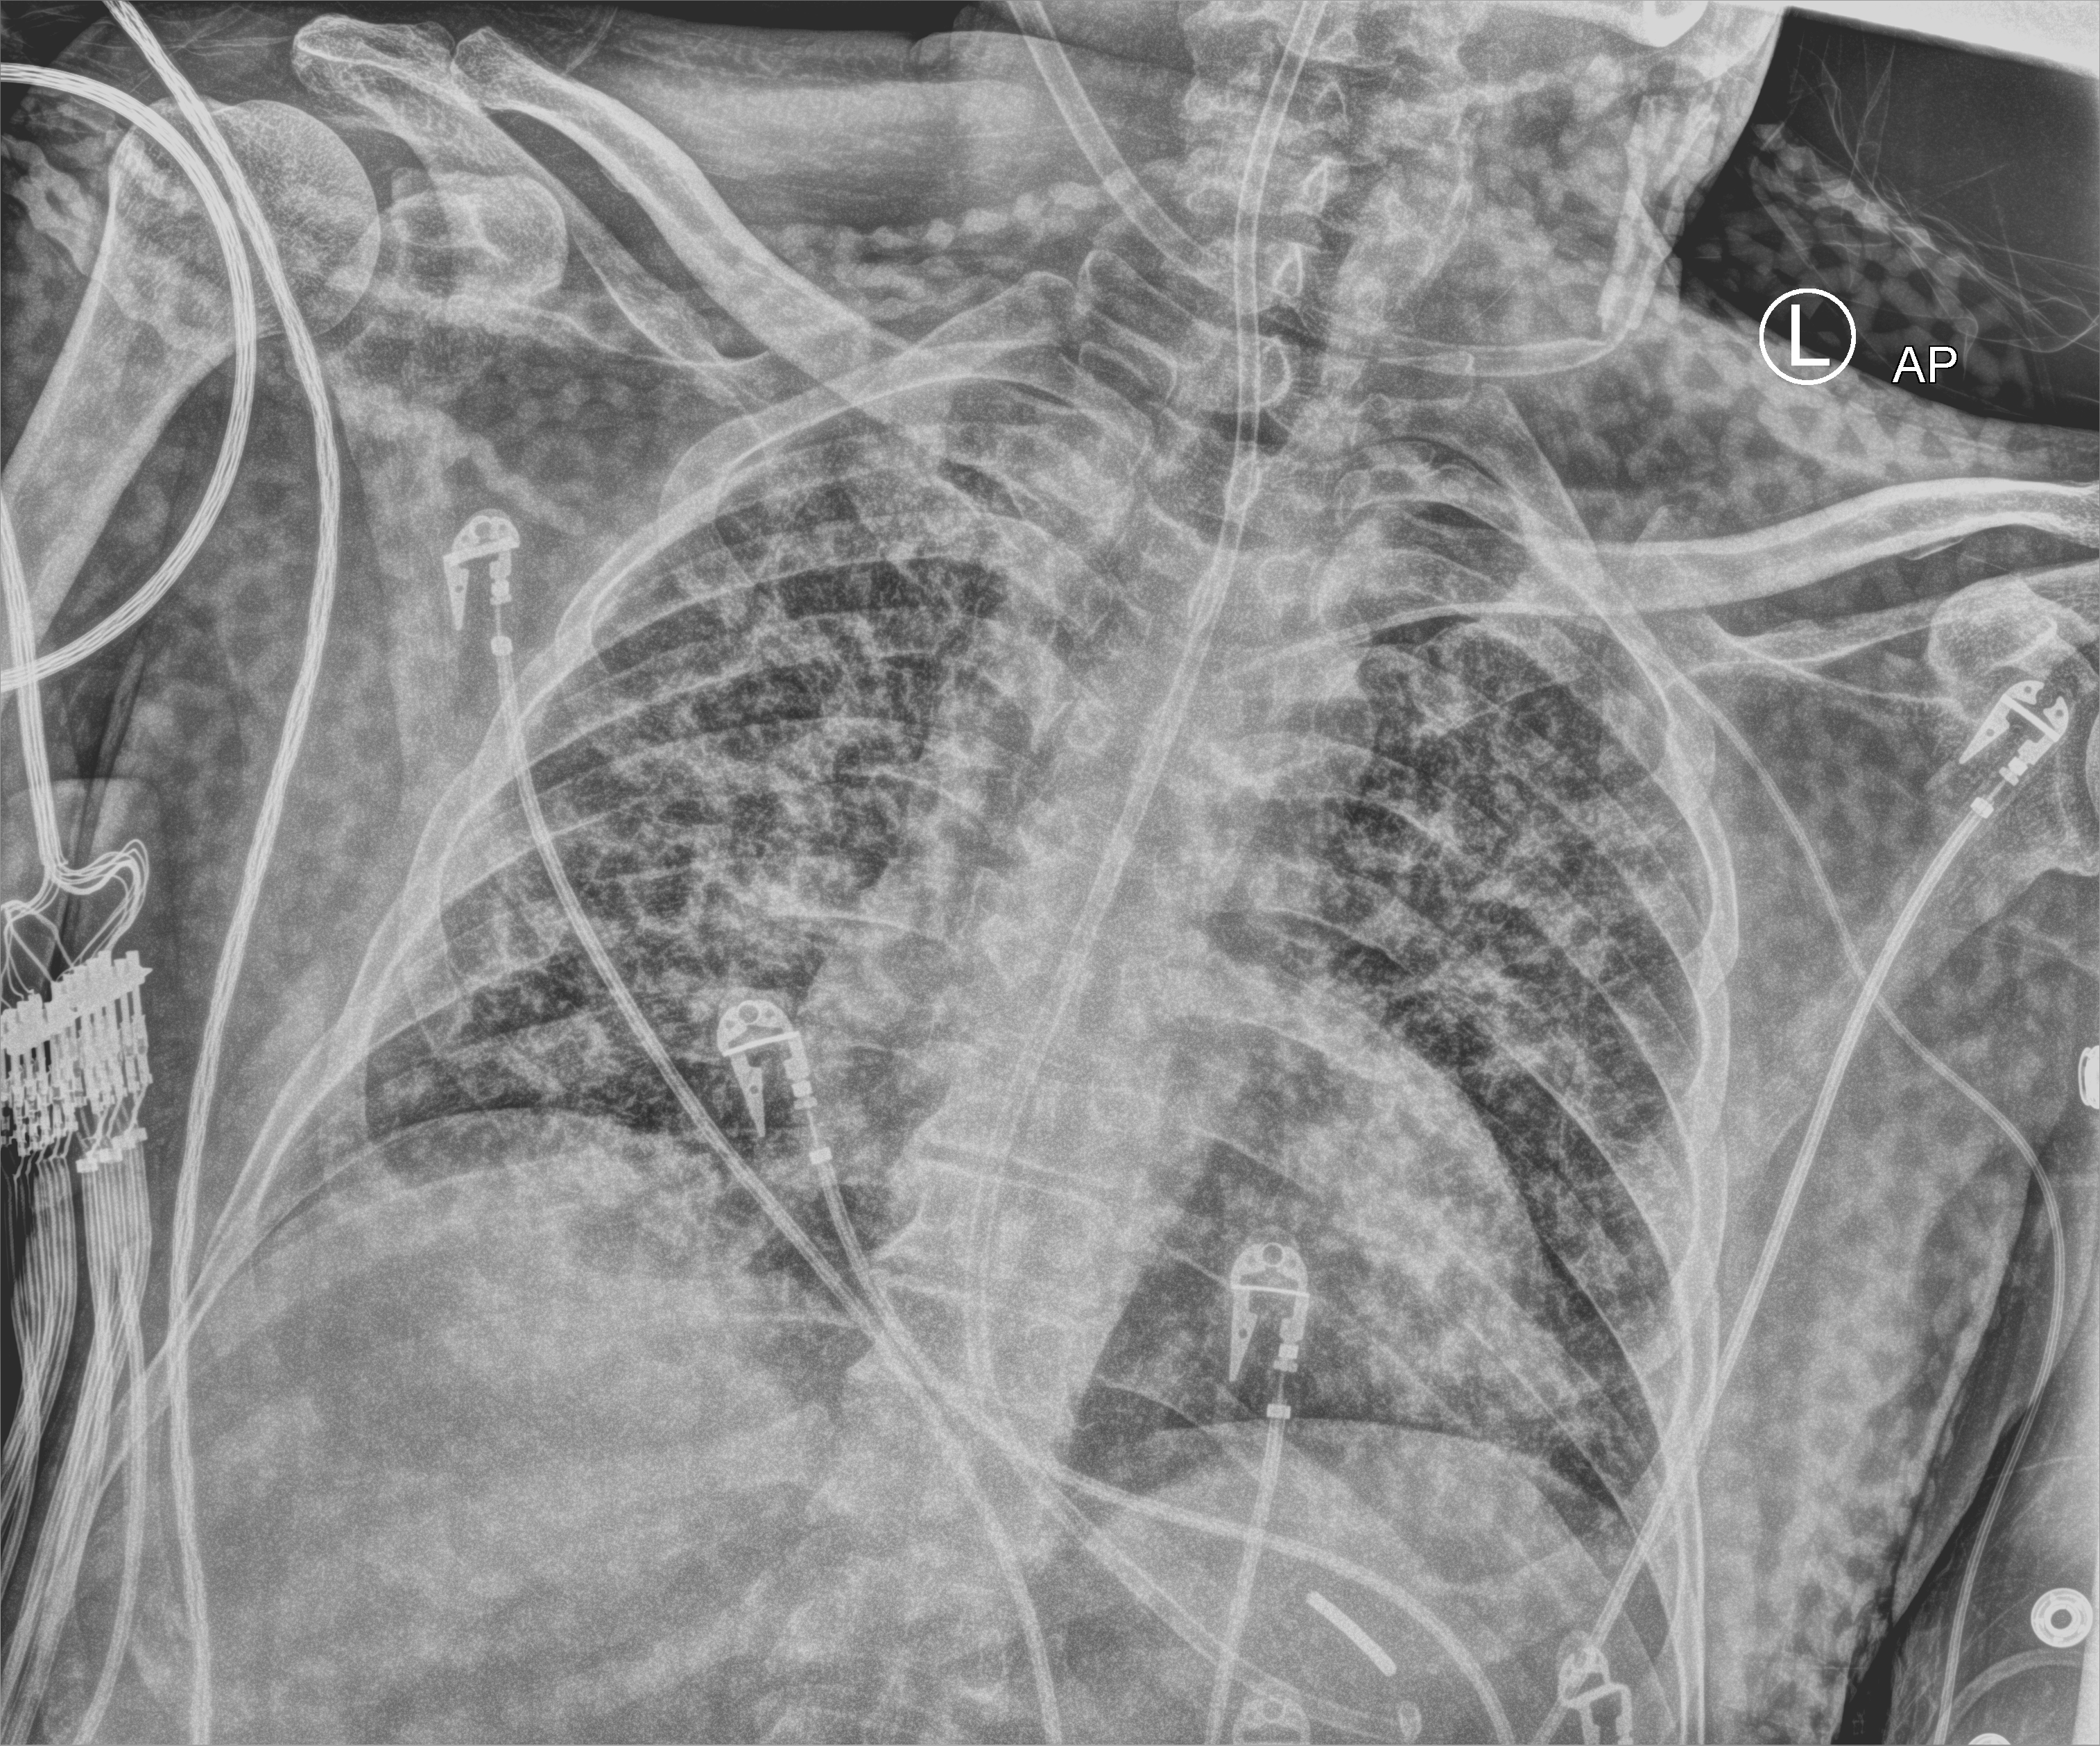
Portable chest radiograph, anteroposterior (AP) projection. Male patient hospitalised with COVID-19, age 18–59 years.
Hospital-stay facts (about this admission, not read from this image; timing relative to this image not recorded): length of hospital stay: 32 days.